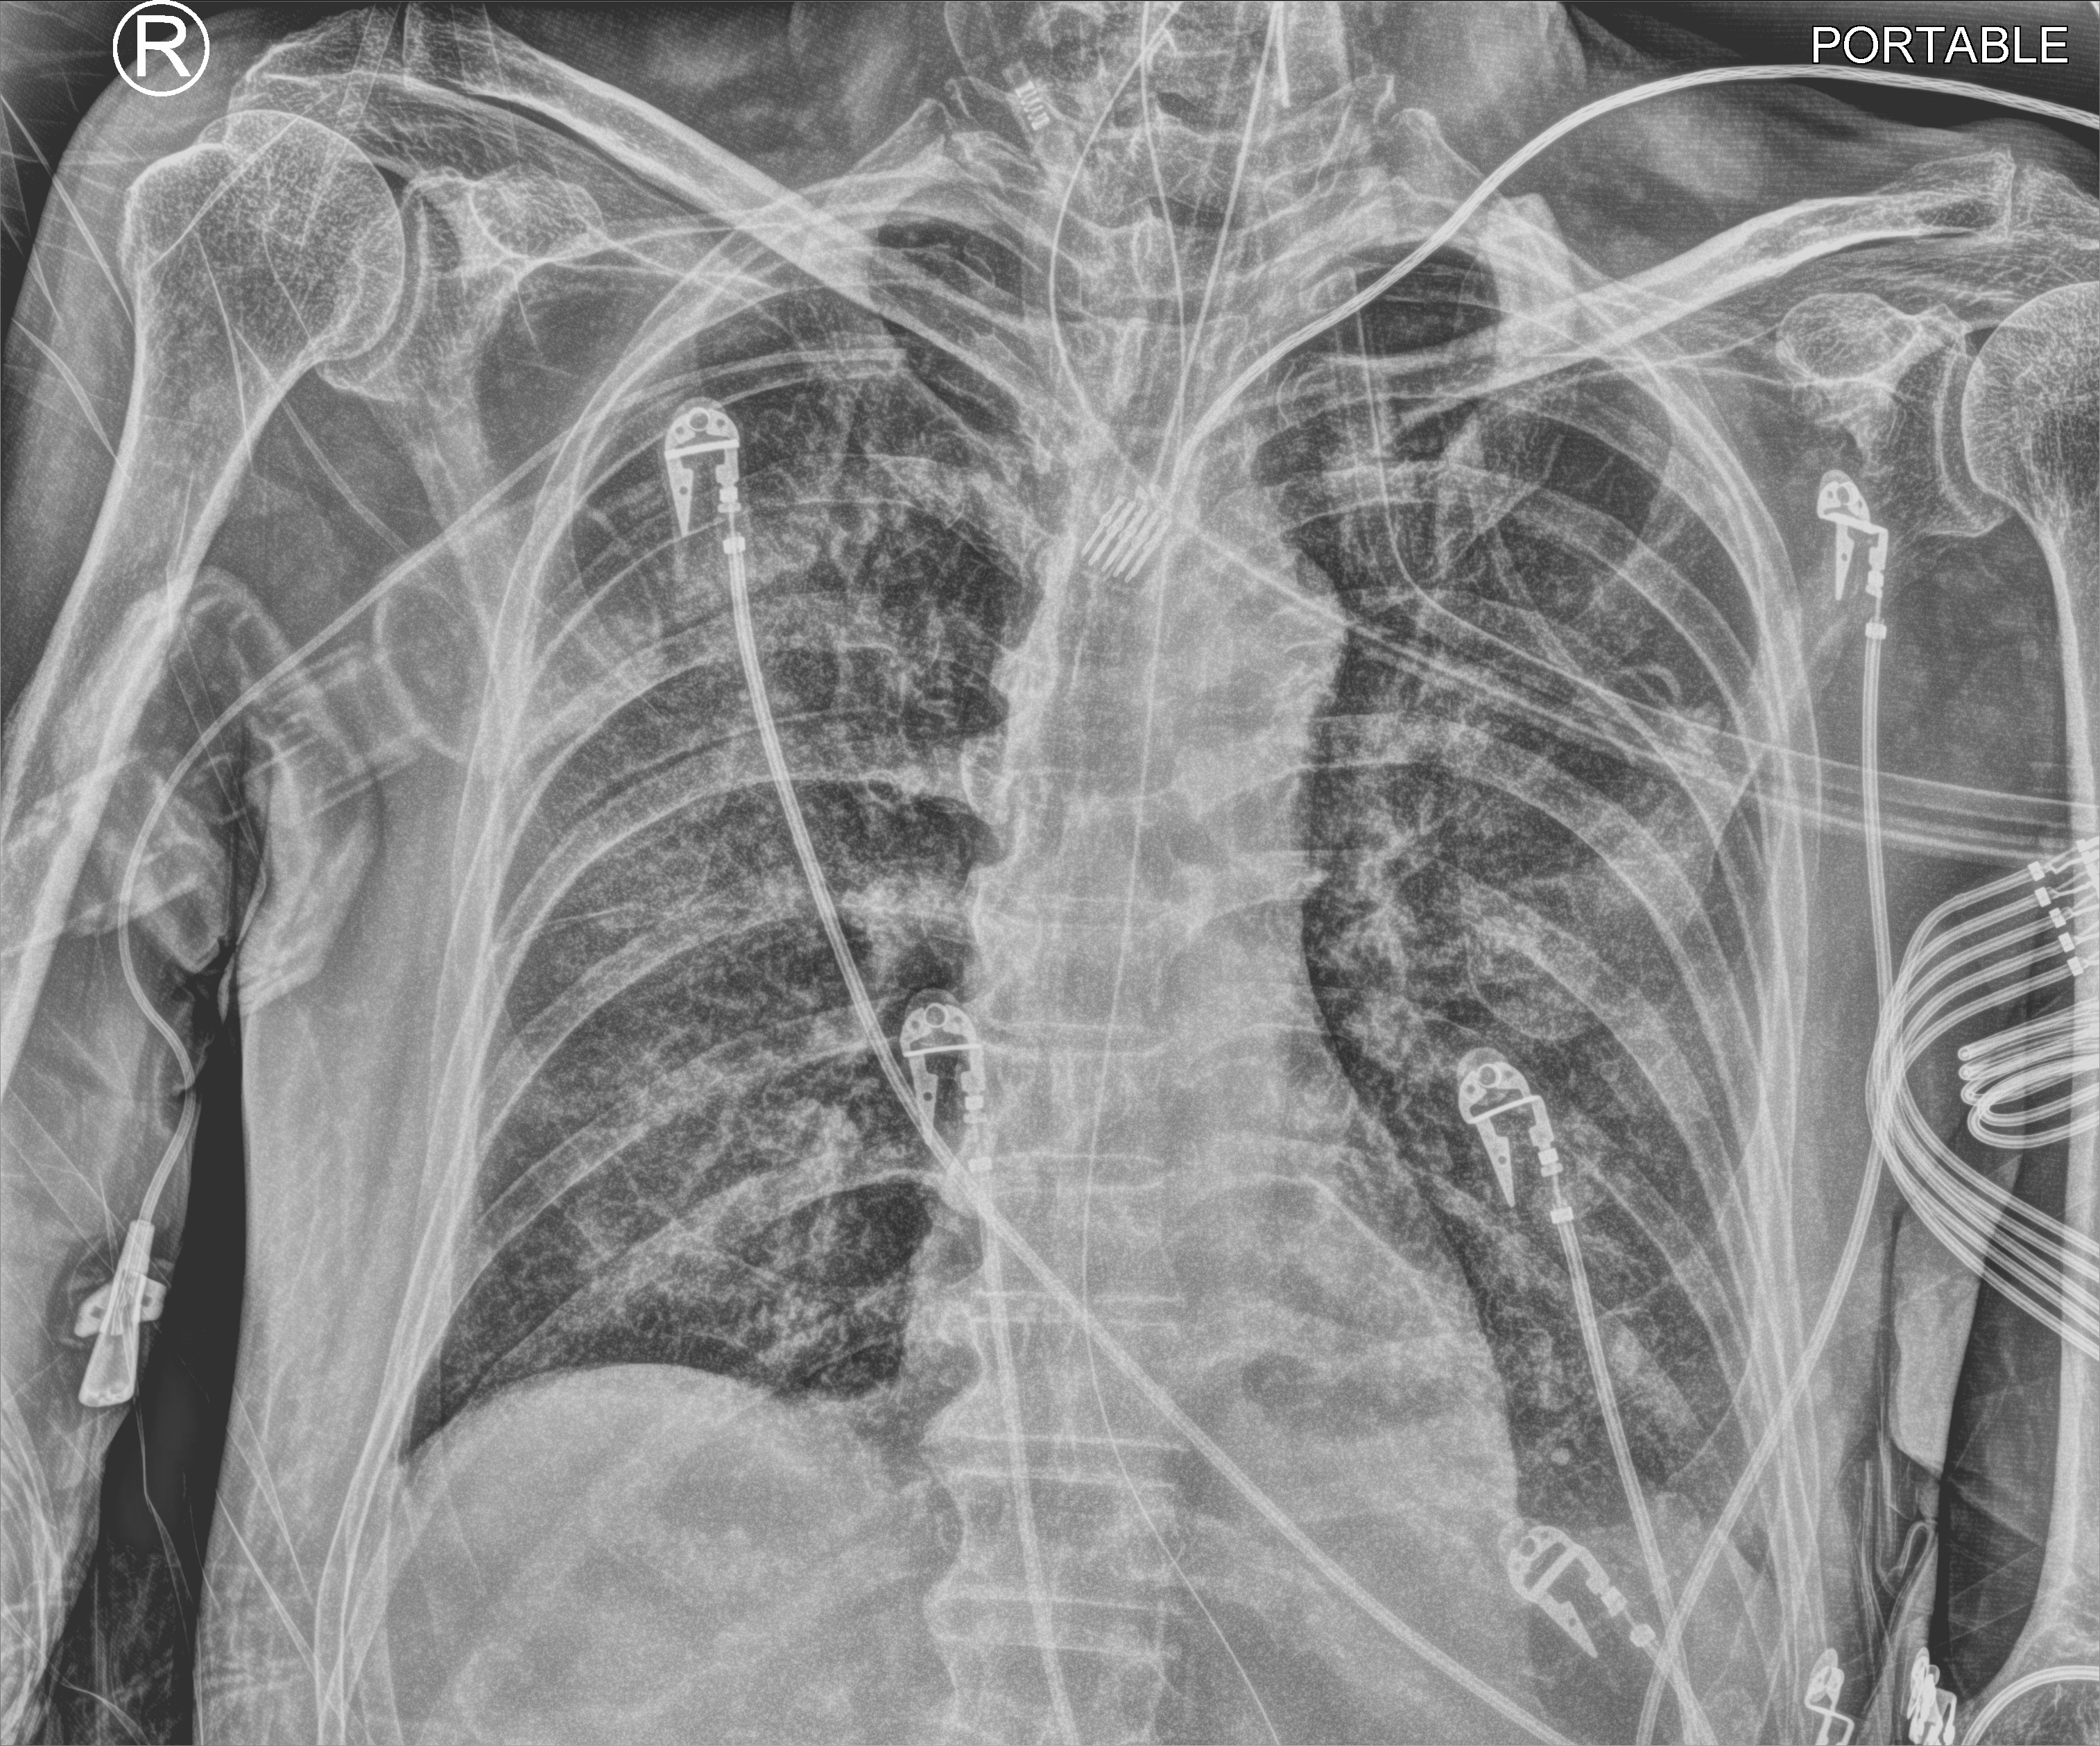
Chest X-ray (portable); anteroposterior (AP) projection. Male patient hospitalised with COVID-19, age 60–74 years.
Hospital-stay facts (about this admission, not read from this image; timing relative to this image not recorded): hypertension (admission record): yes; length of hospital stay: 42 days.